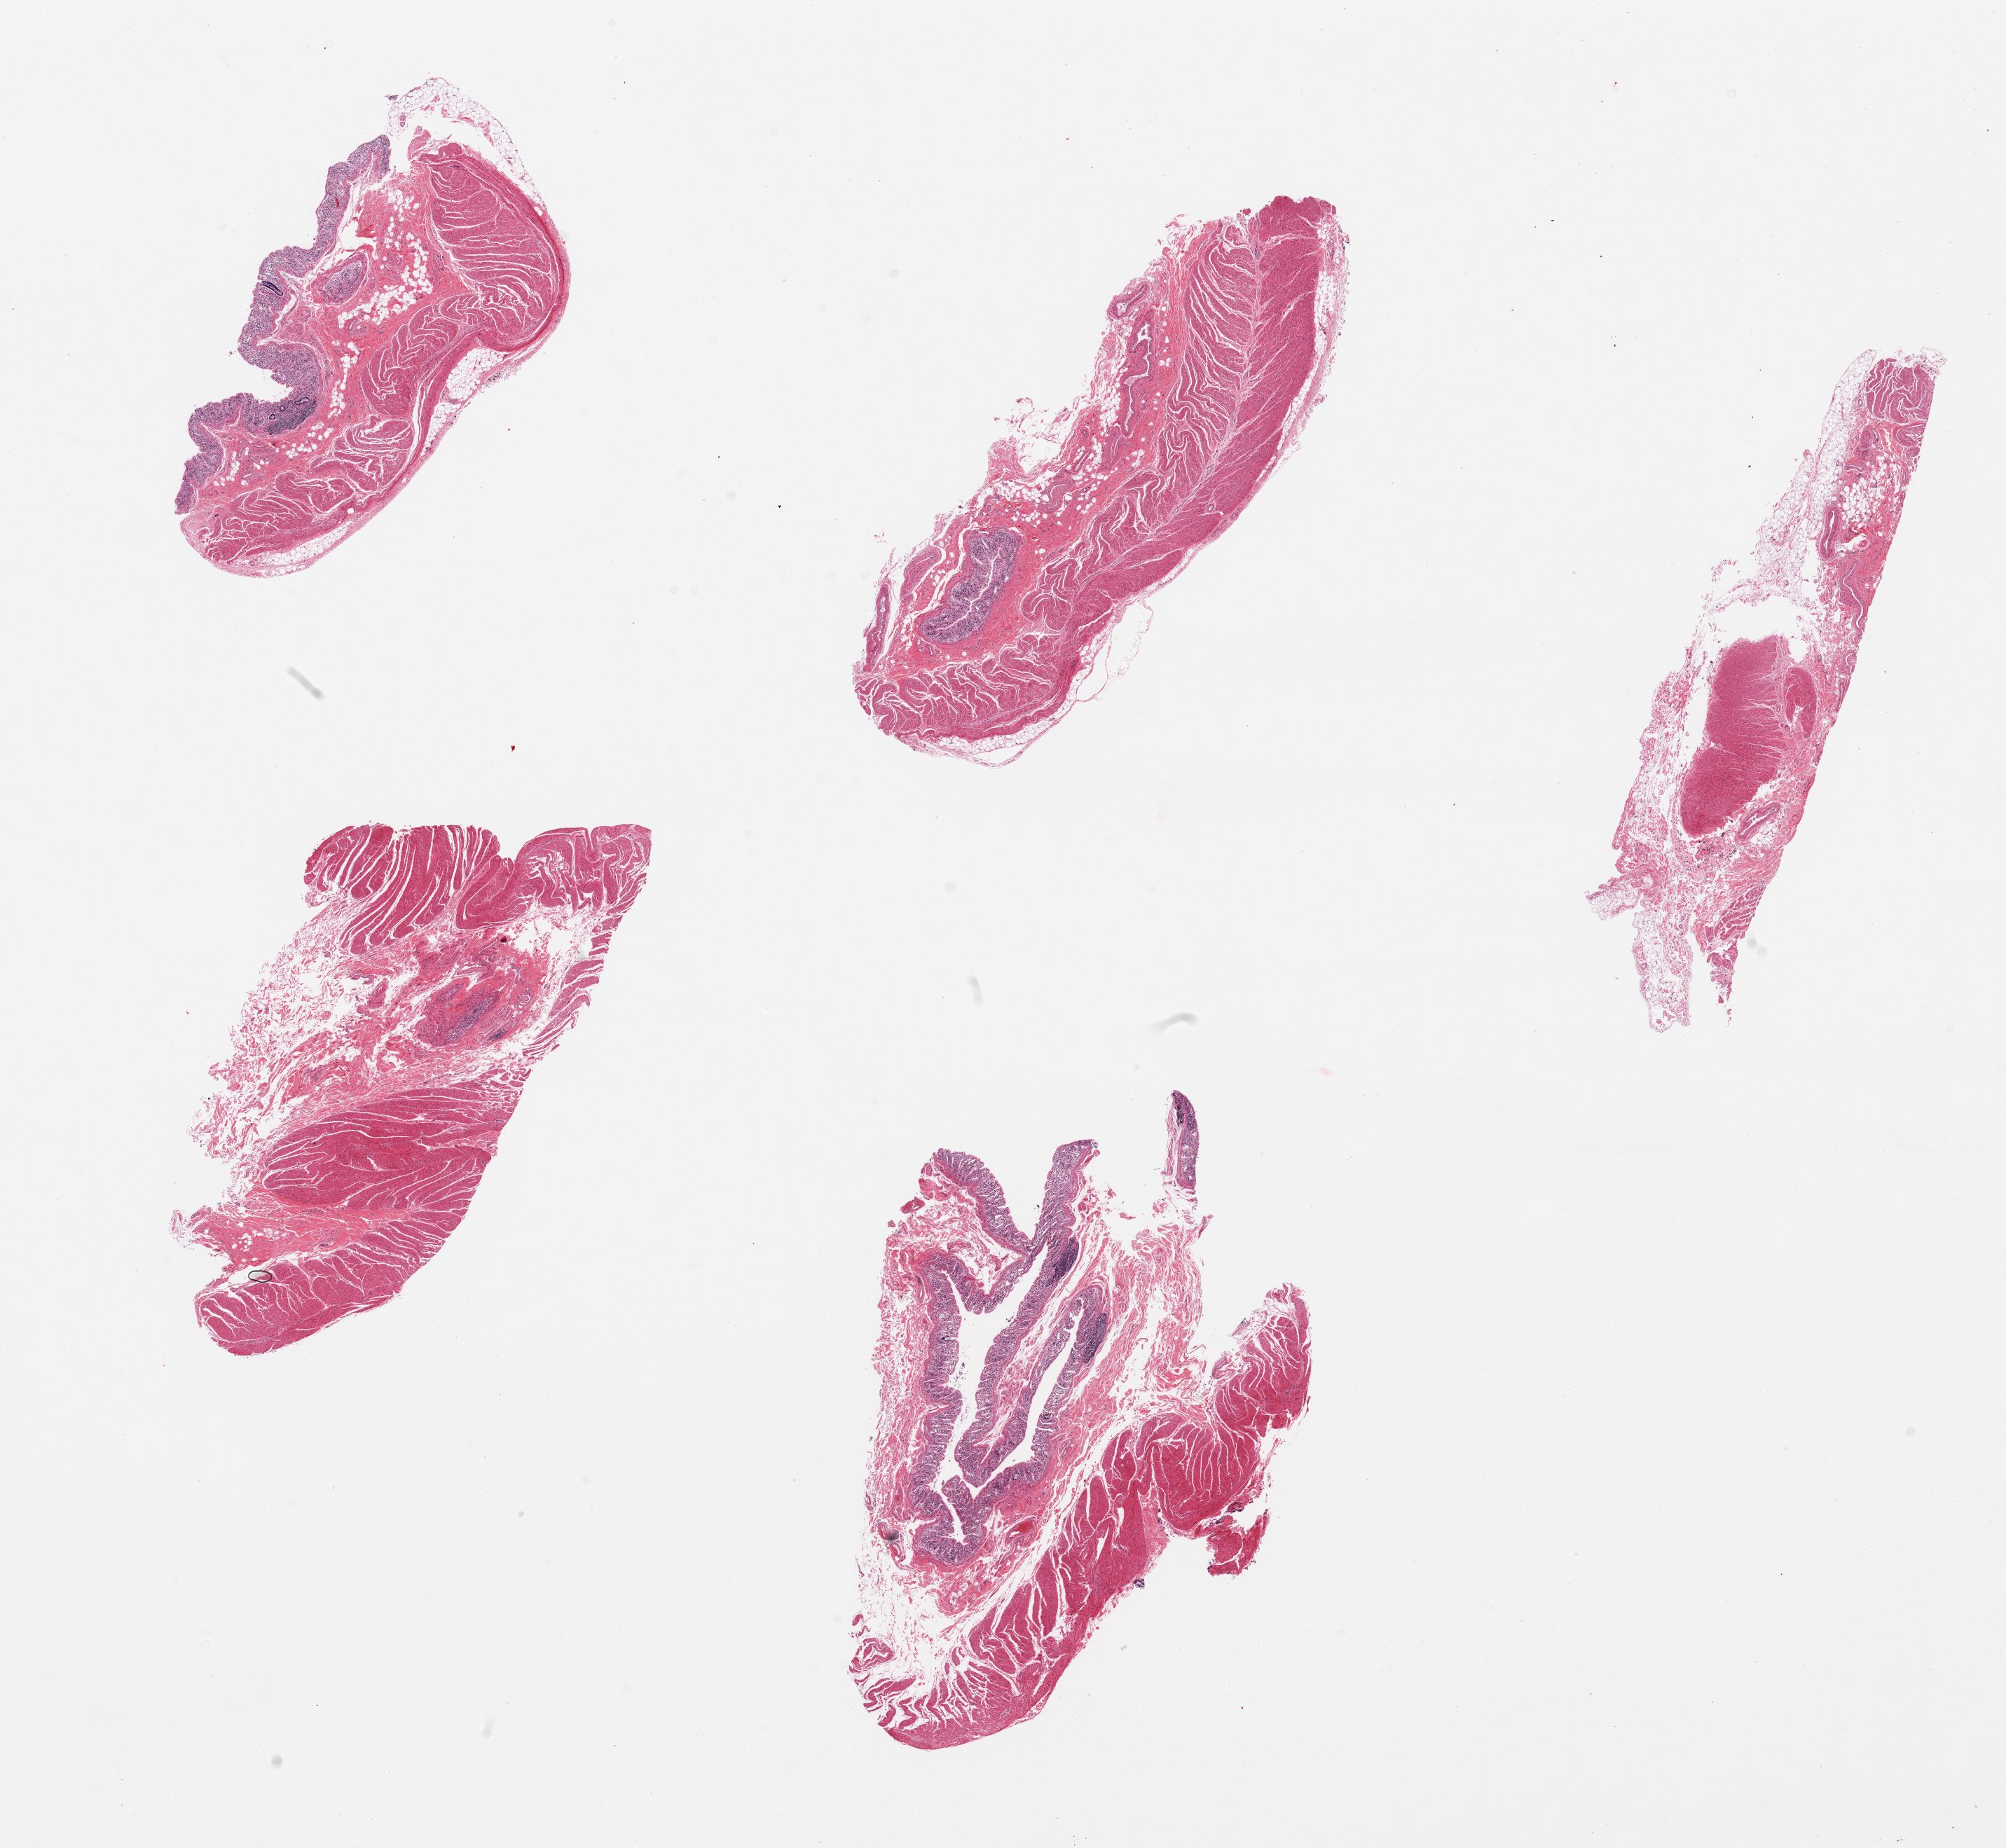
Digitized H&E-stained section, a low-resolution overview of the entire scanned area, about 22.6 x 20.9 mm (acquisition: 20x scan). Donor sex: female.
• specimen: PAXgene-fixed paraffin-embedded (PFPE) section; target tissue: transverse colon; tissue donor sample